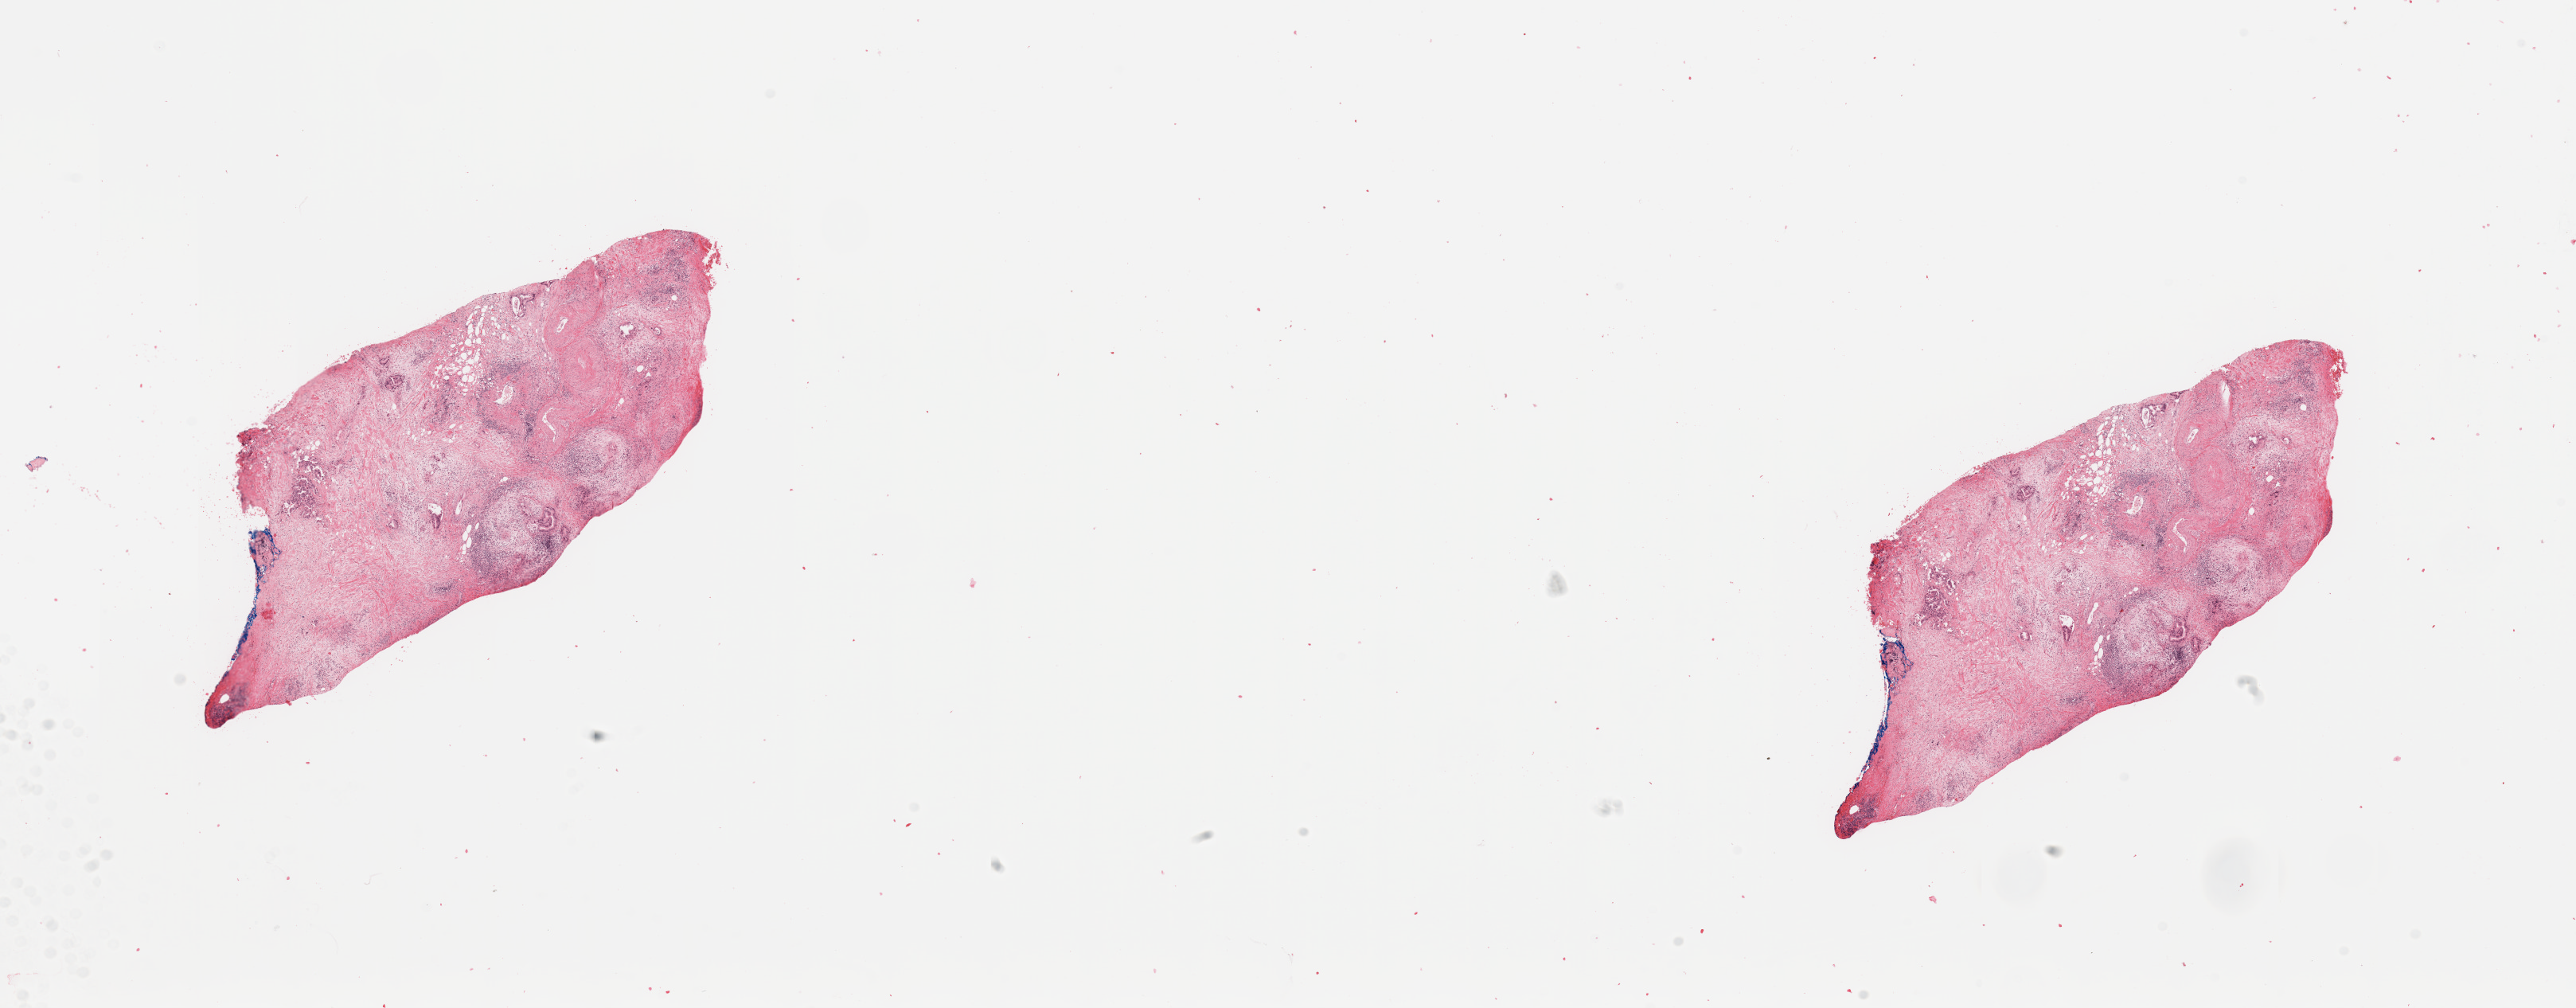
H&E whole-slide image — a low-resolution overview of the entire scanned area, about 25.6 x 10.0 mm (from a 20x scan), tumour tissue sample, pancreas. 77-year-old female patient. Histologic grade: G2 (moderately differentiated).
- primary tumour site (as recorded): head
- AJCC pathologic stage: IIB
- histologic diagnosis: Infiltrating duct carcinoma, NOS